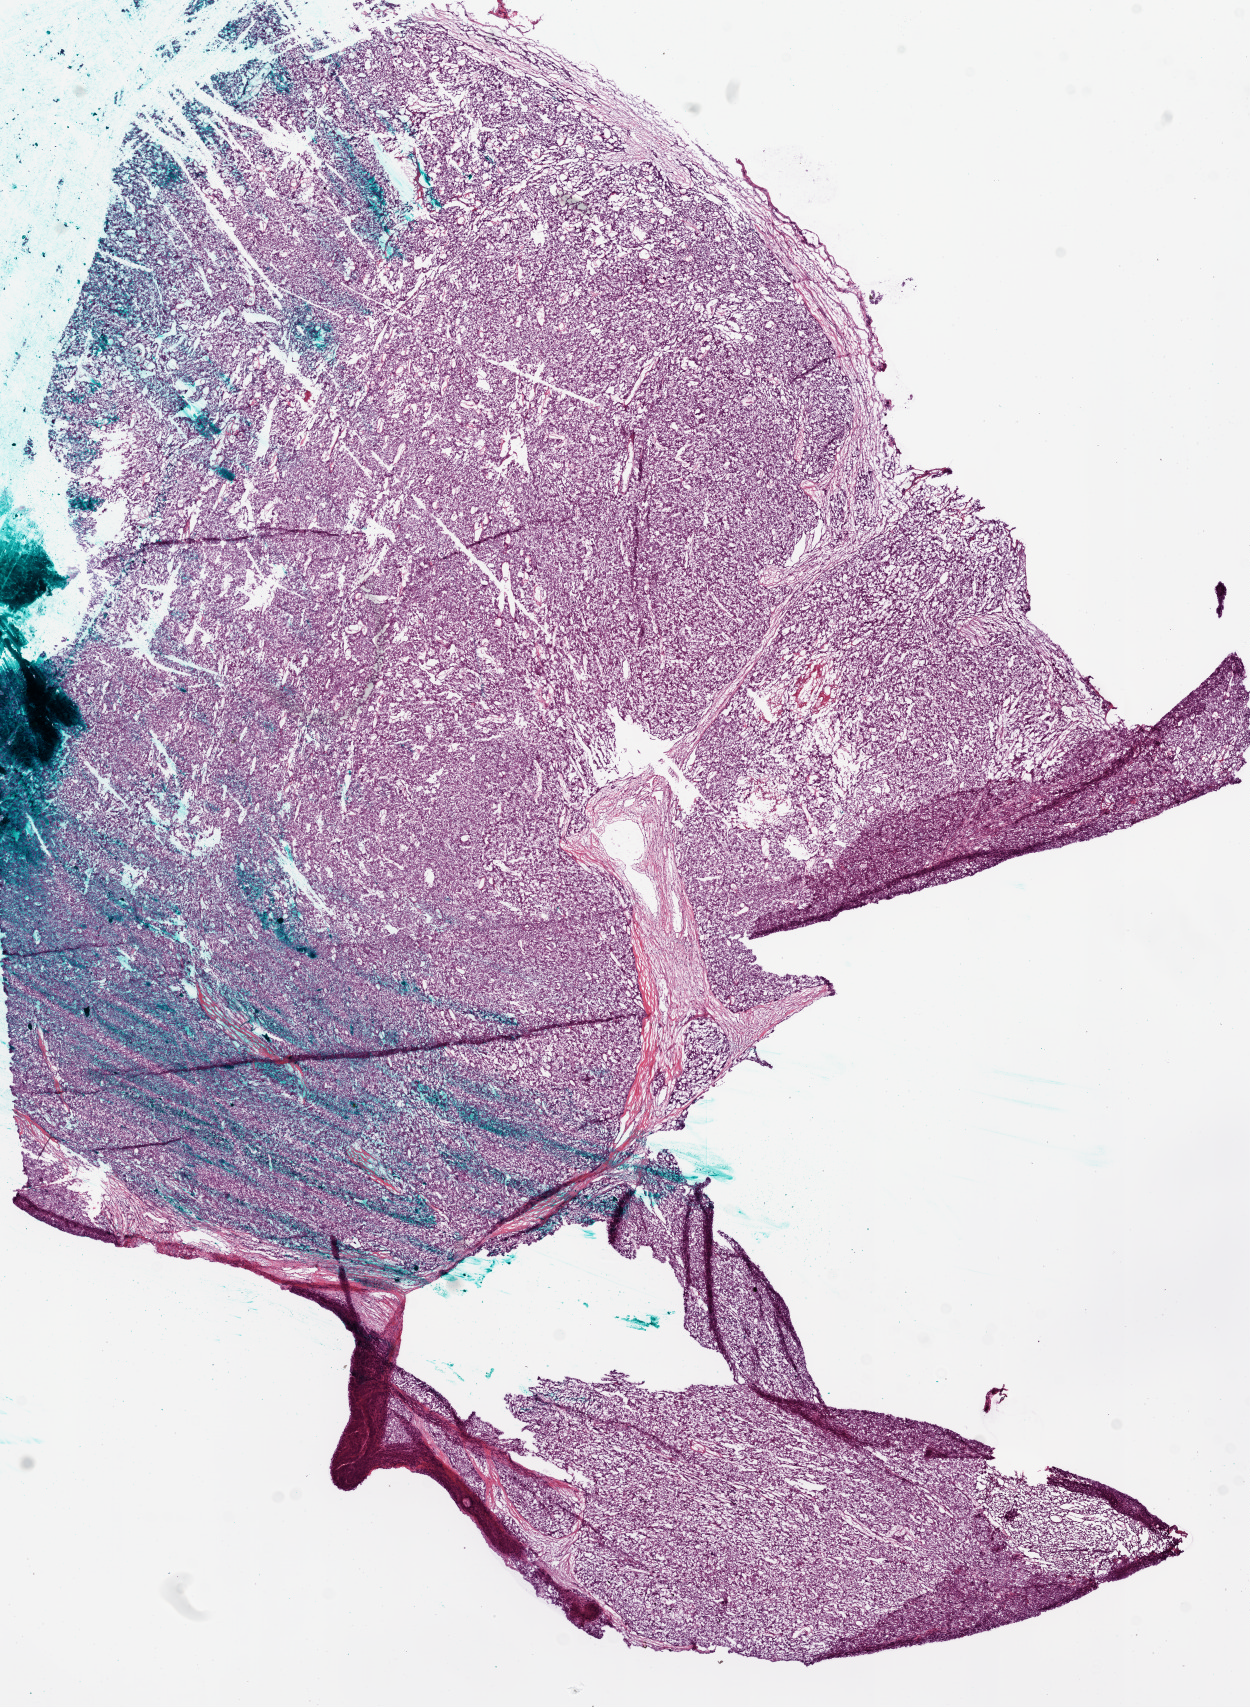
Whole-slide histology image, H&E-stained — whole scanned area (about 10.0 x 13.7 mm) shown as a low-resolution overview, frozen section, sample: primary tumour, ovary. Female patient; age at initial diagnosis 60 years. Histologic grade: G3 (poorly differentiated). Composition of this section per pathologist review: tumour cells 98%, tumour nuclei 99%, normal cells 0%, stromal cells 1%, necrosis 1%.
Laterality: left. FIGO stage: IIIC. Pathologic diagnosis: Serous cystadenocarcinoma, NOS.